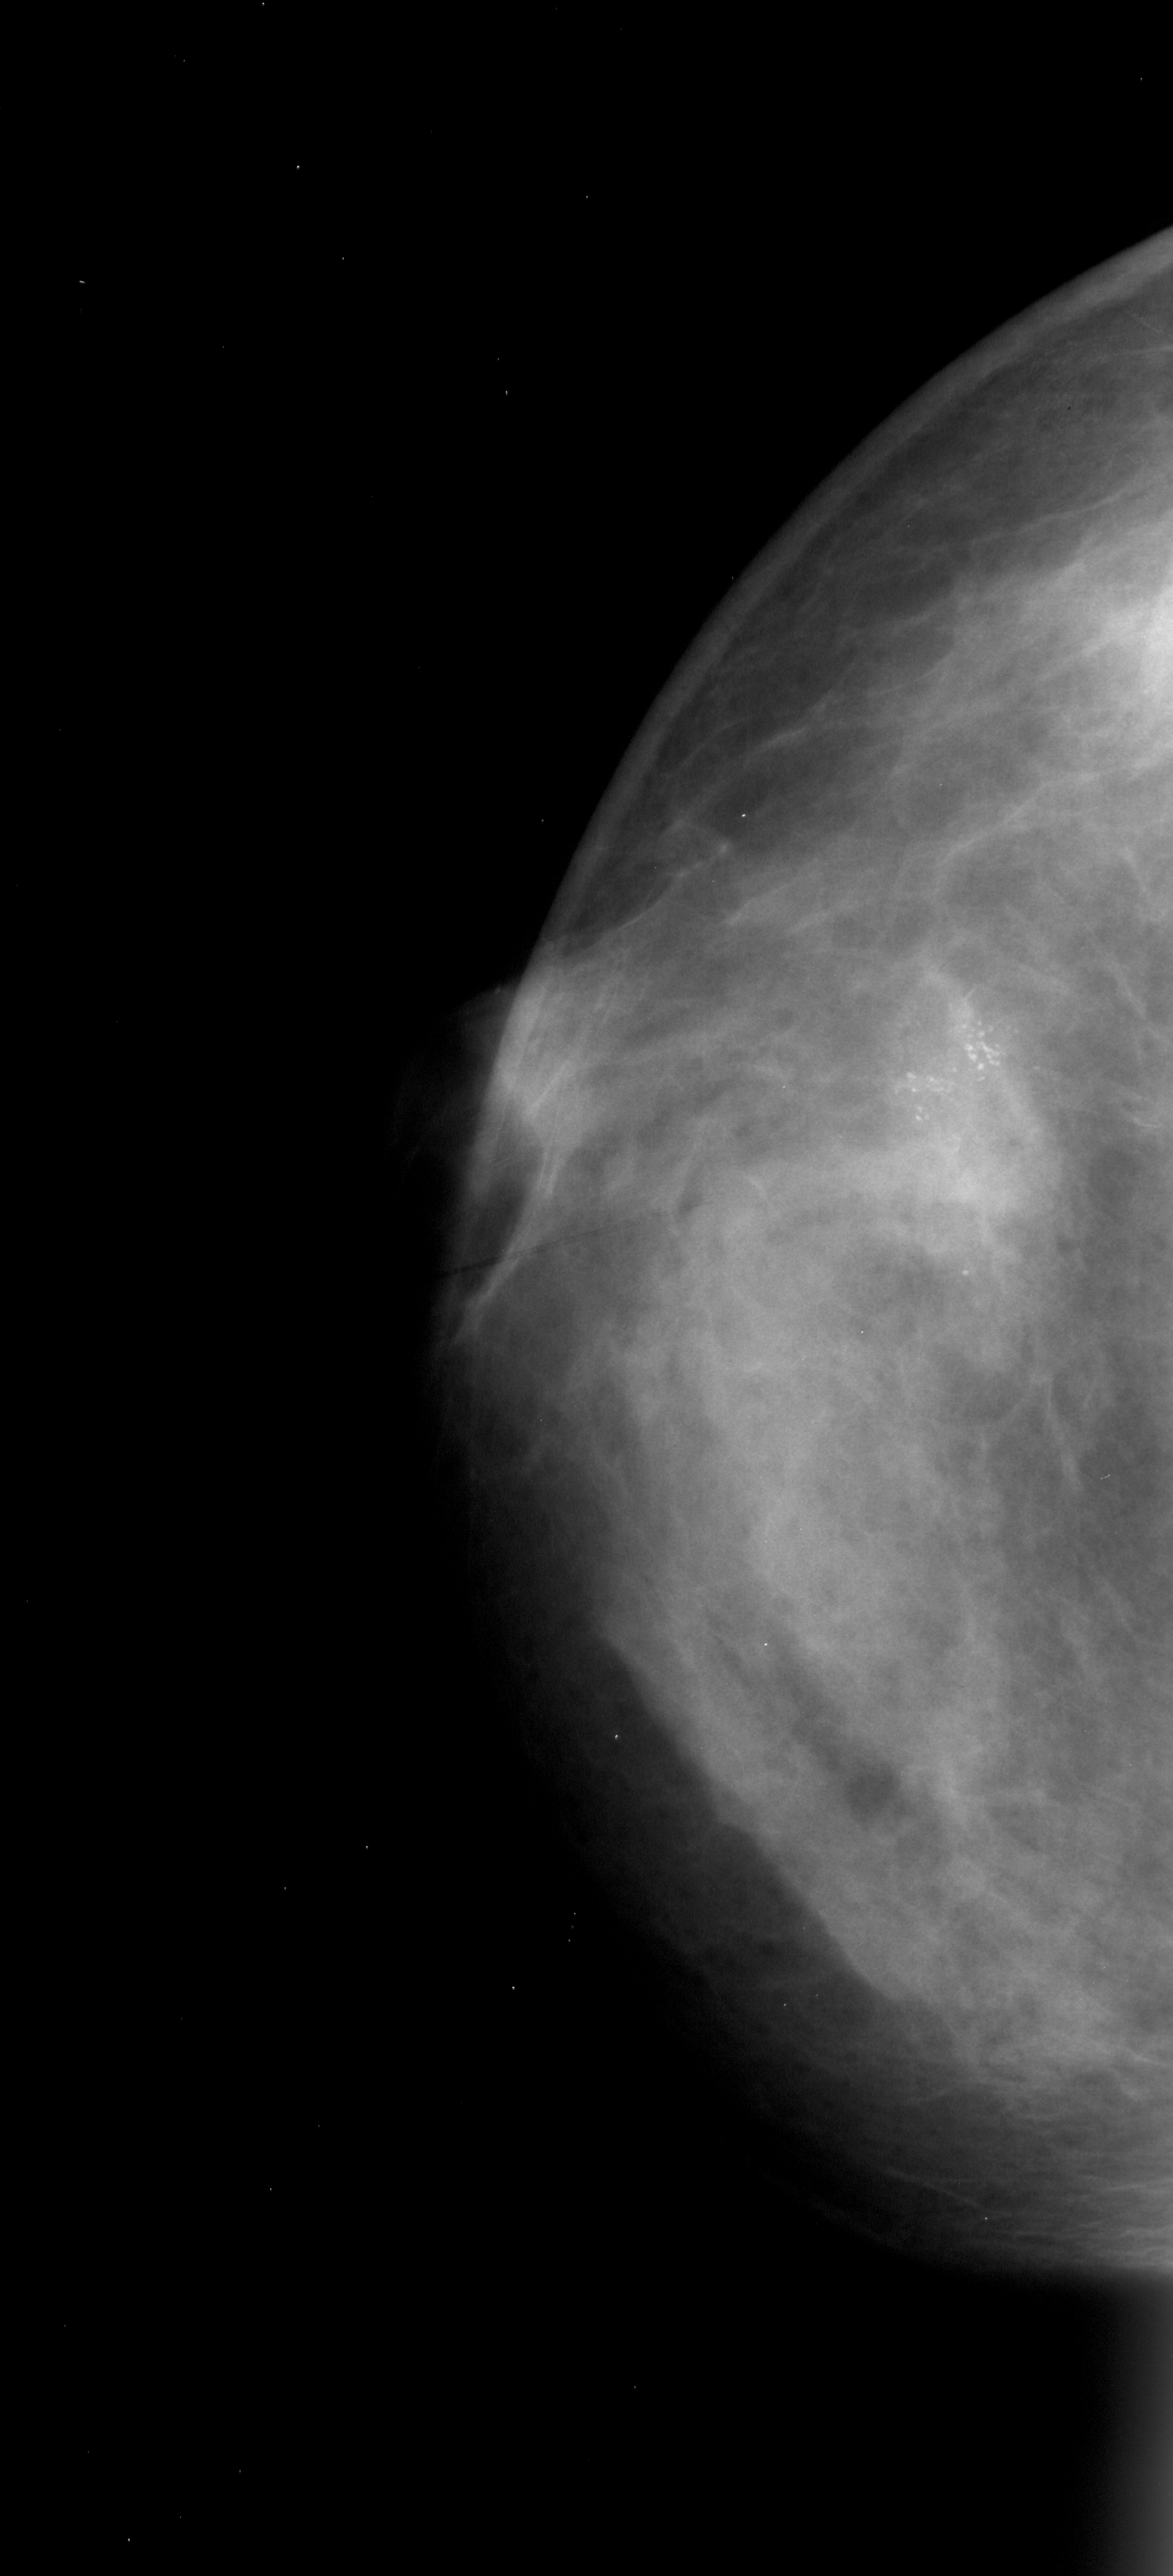
Scanned film-screen mammogram; left breast; CC view; 1173 × 2576 image matrix.
Expert-marked regions of interest on this film, with their recorded descriptors:
- calcifications, morphology pleomorphic, distribution clustered; BI-RADS assessment category 4; subtlety rating 5 on a 1 (subtle) to 5 (obvious) scale; pathology result (as recorded, not read from the image): malignant: bounding box [x1, y1, x2, y2] px = [878, 975, 1059, 1168]